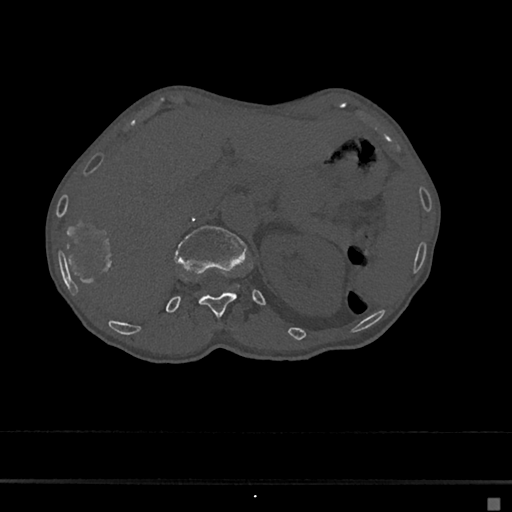
CT including the spine, one axial slice. Position 109 of 797 along the scan axis. Bone window (W 1800 / L 400 HU). 512 × 512 image matrix, field of view 360 × 360 mm. Female patient, age 68 years. From the clinical record (not read from this slice): primary cancer: renal.
Outlined on this slice (semi-automatically segmented with operator editing):
- L1 vertebra: box from (x=174, y=226) to (x=248, y=269) px
- T12 vertebra: (x=198, y=291)–(x=237, y=317)